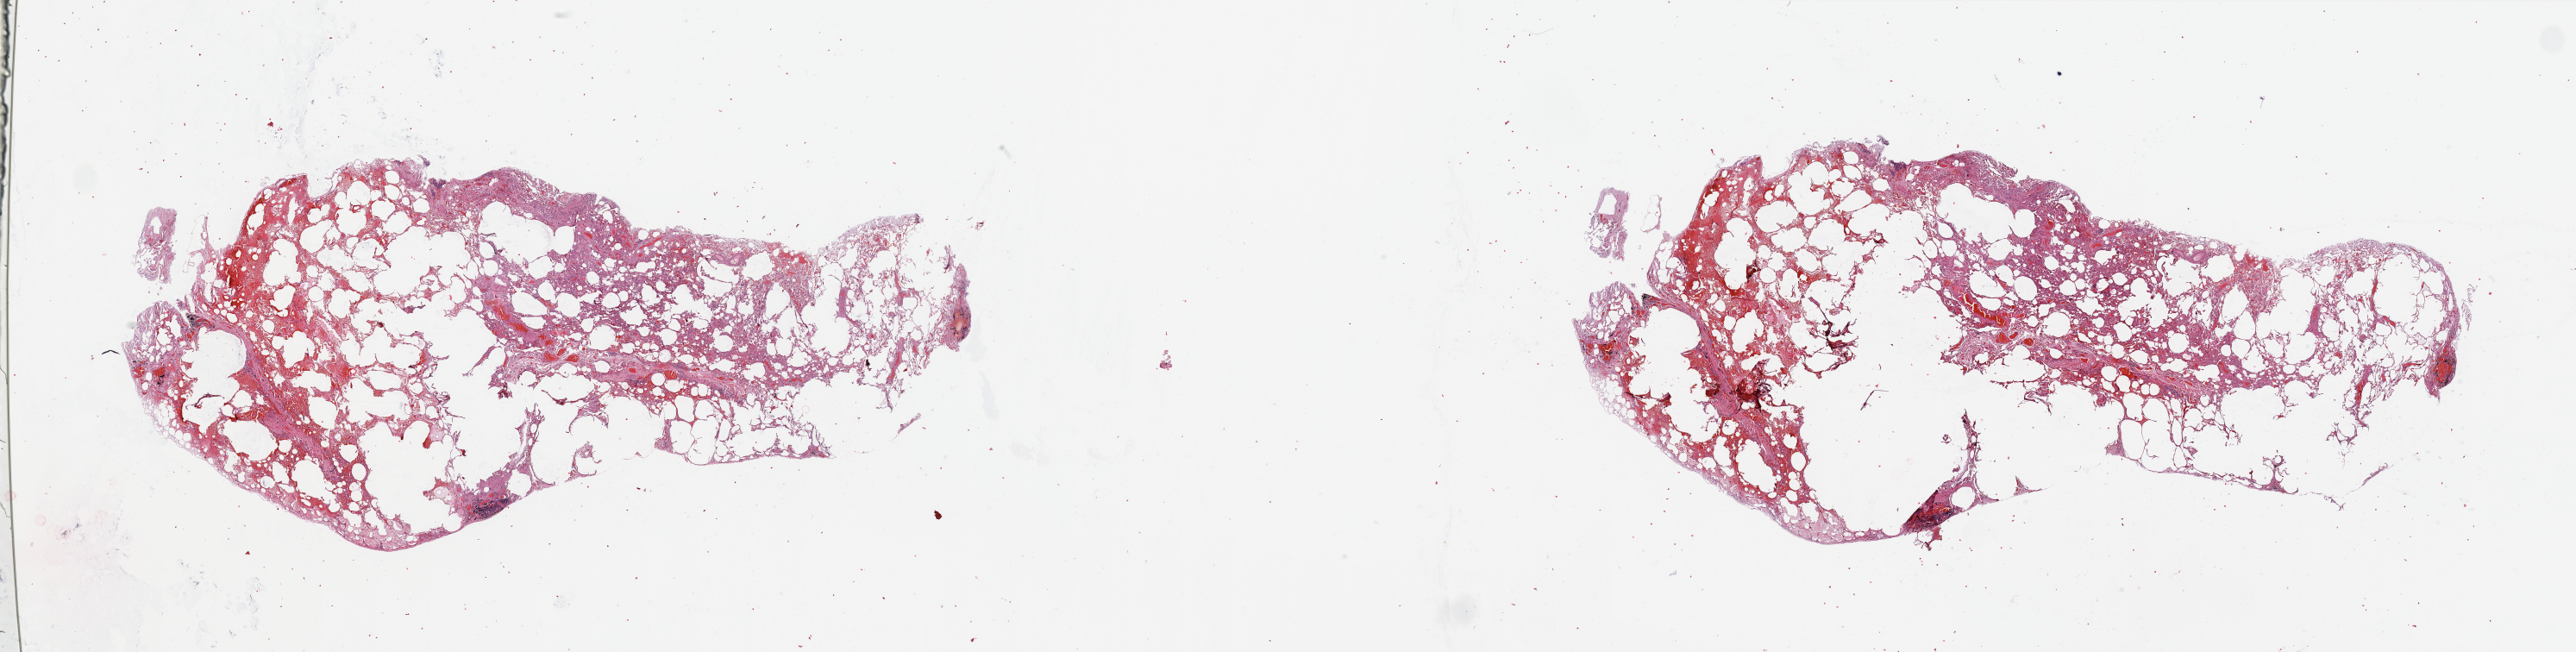
Whole-slide histology image, H&E, low-resolution overview of the scanned area, about 47.3 x 12.0 mm (slide scanned at 20x), normal (non-tumour) tissue sample, sampled site: lung. Patient: male, age 62 years.
This section: normal (non-tumour) tissue from the same patient. Patient diagnosis: Squamous cell carcinoma, NOS.